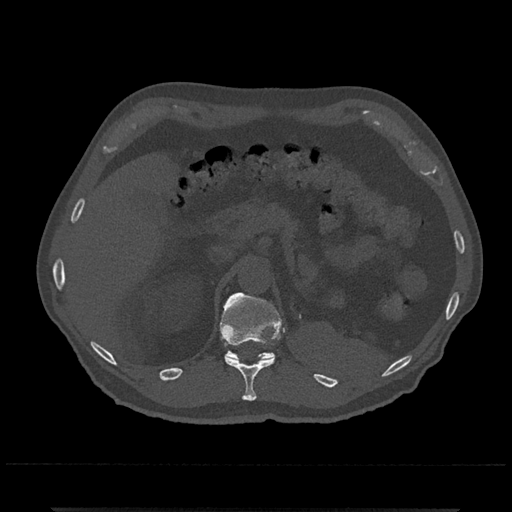
CT including the spine, one axial slice. Position 463 of 797 along the scan axis. Reconstruction kernel Br40s/3. 120 kVp. Bone window (W 1800 / L 400 HU). 0.5 mm slice thickness. 512 × 512 image matrix. Patient: male, 67 years. Case-level facts recorded for this patient, not image findings: primary cancer: prostate.
Annotated regions visible in this slice (semi-automatically segmented with operator editing):
- T11 vertebra: bounding box [x1, y1, x2, y2] px = [225, 356, 275, 401]
- T12 vertebra: [220, 293, 285, 361]